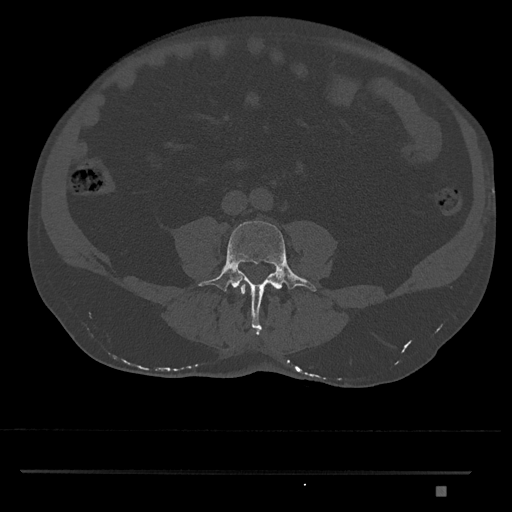
CT including the spine, one axial slice; position 622 of 1134 along the scan axis; reconstruction kernel Br40s/3; bone window (W 1800 / L 400 HU); 512 × 512 image matrix. Male patient, age 65 years. From the clinical record (not read from this slice): primary cancer: prostate.
Structures marked on this image (semi-automatically segmented with operator editing):
- L3 vertebra: bounding box <239,283,276,295> (left, top, right, bottom; pixels)
- L4 vertebra: <198,221,317,334>